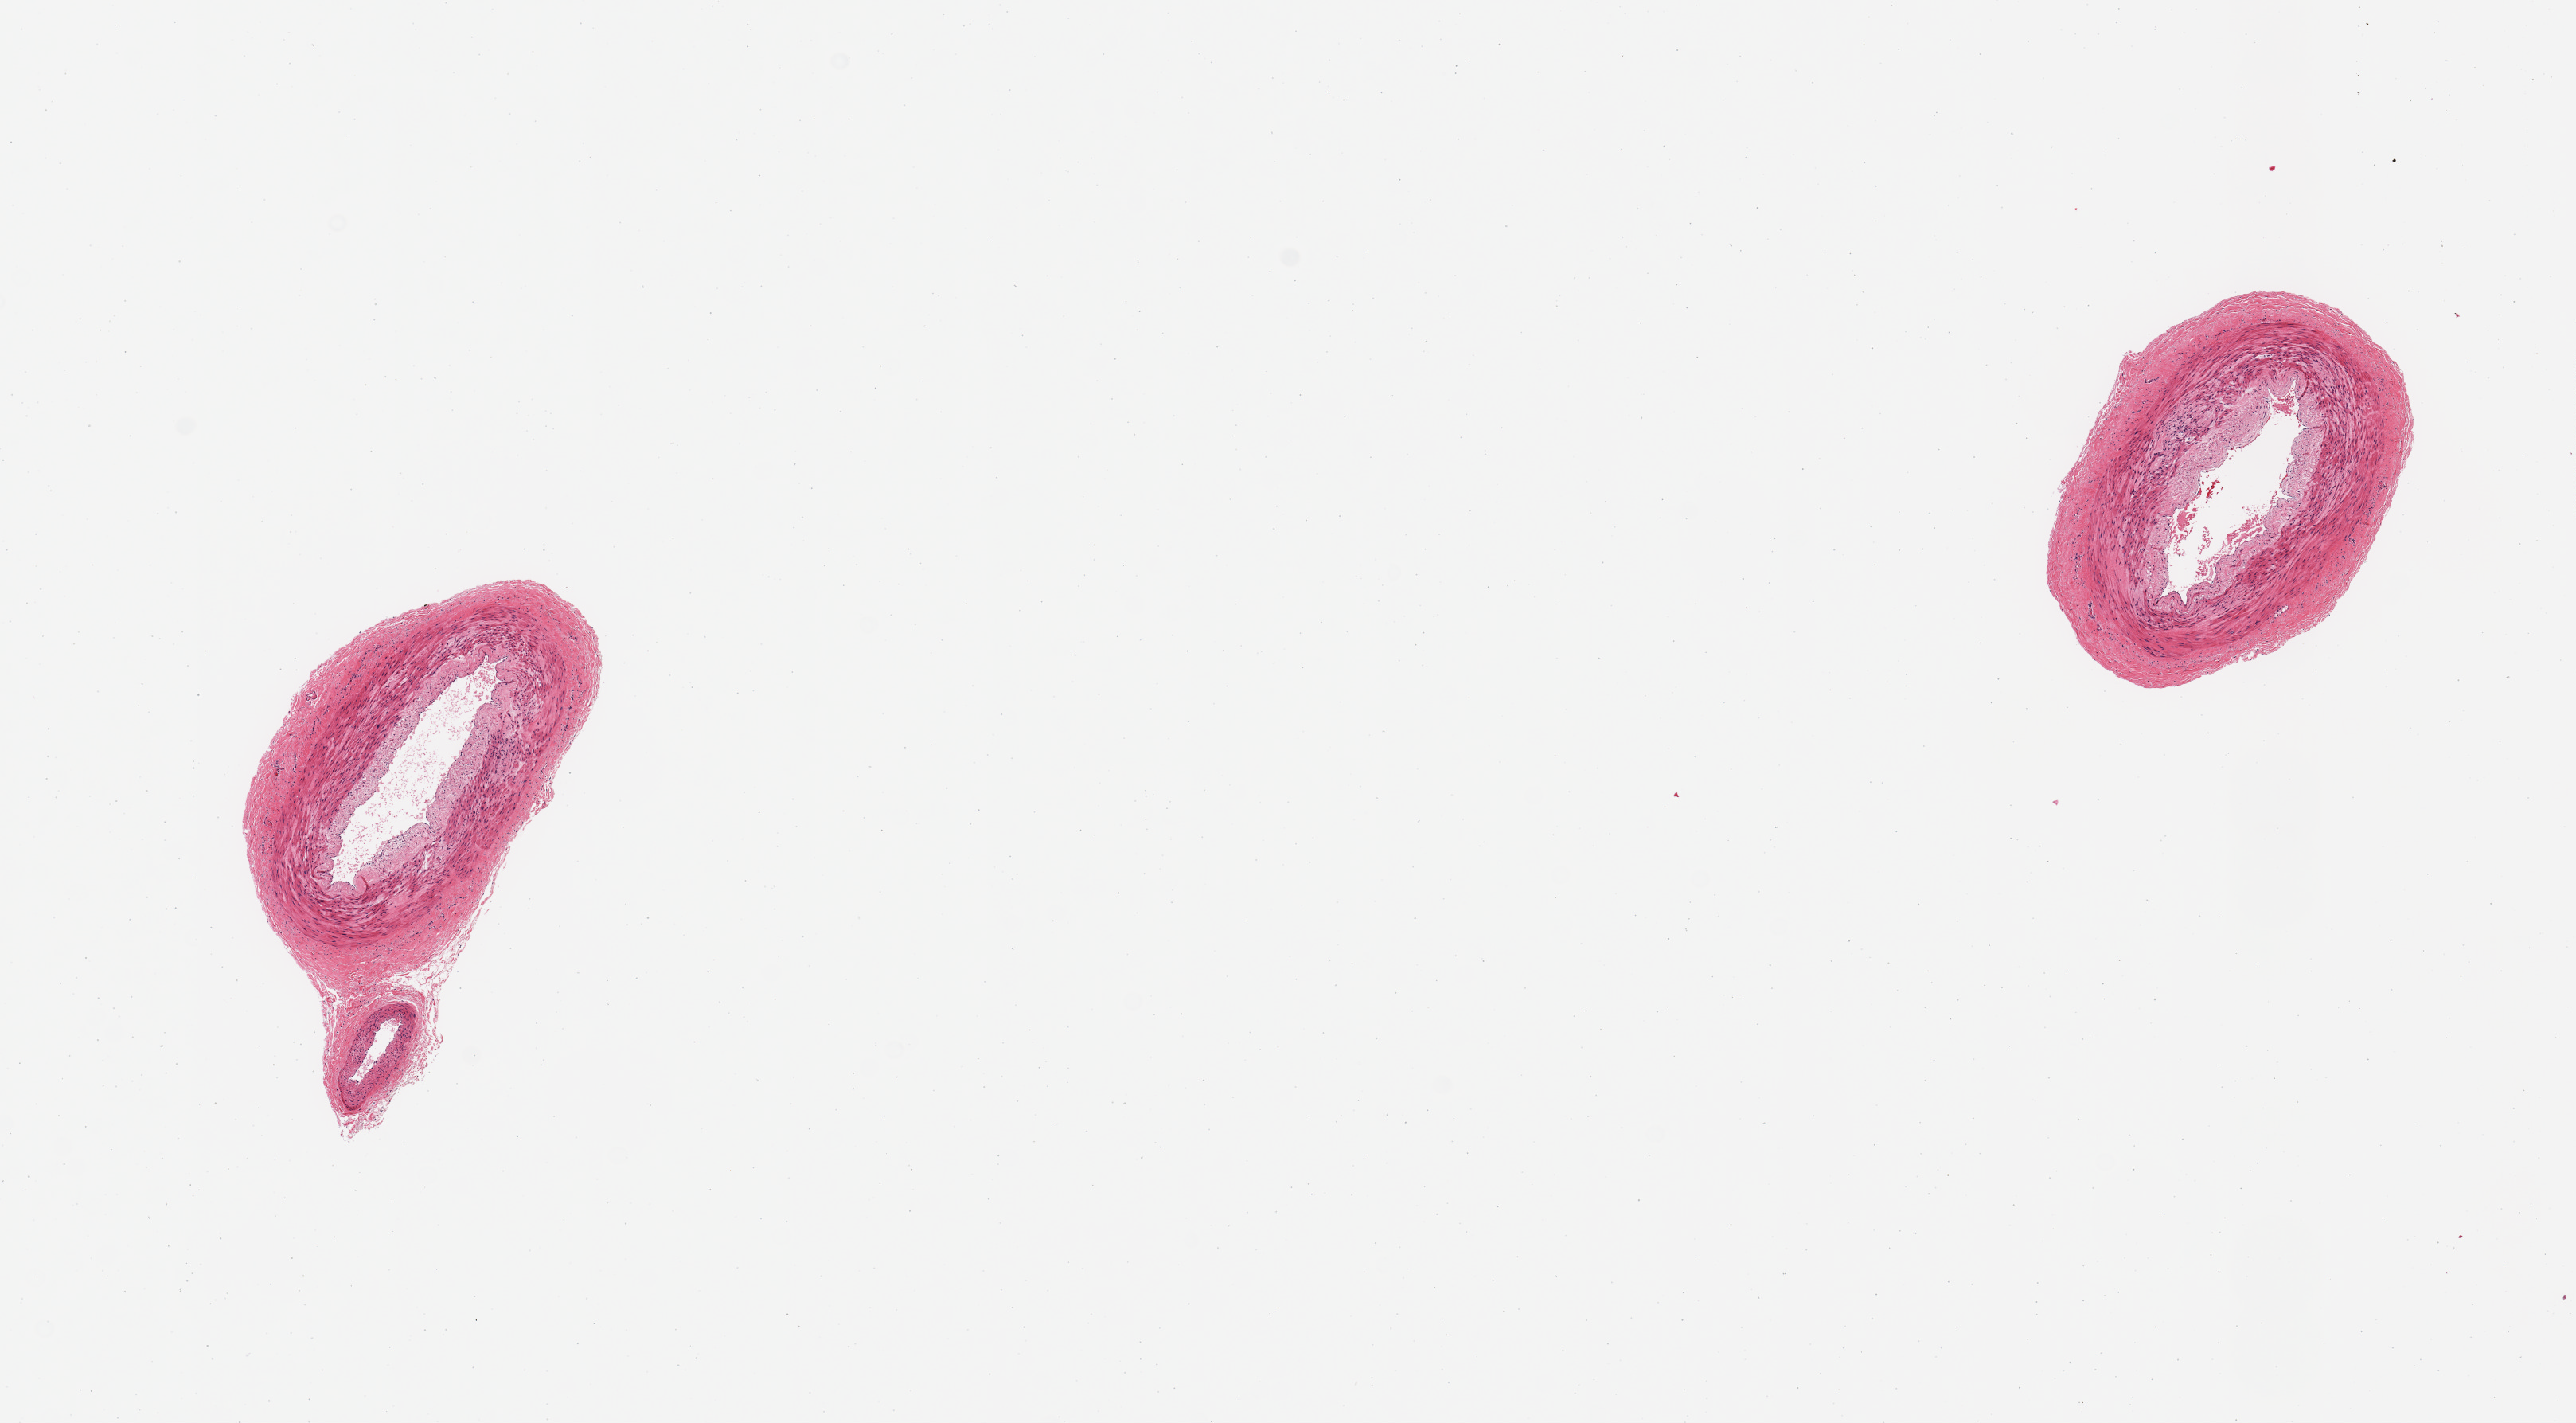
Whole-slide image, H&E stain, brightfield, a low-resolution overview of the entire scanned area, about 12.8 x 7.1 mm; PAXgene-fixed paraffin-embedded (PFPE) section; target tissue: tibial artery; donor tissue sample.
Pathologist's review note for this sample: 2 pieces, no significant atherosis or adherent fat.